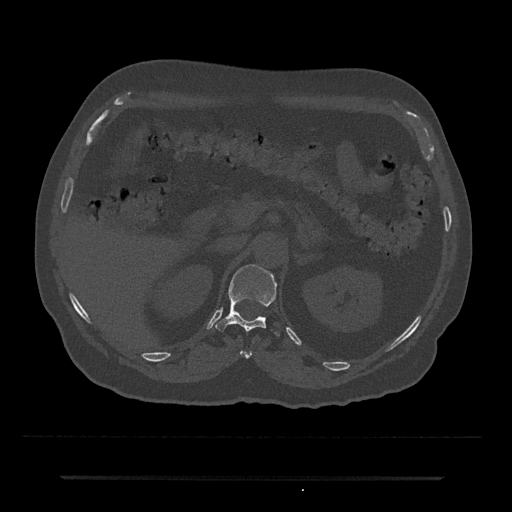
CT including the spine, one axial slice; position 128 of 797 along the scan axis; reconstruction kernel Br40s/3; 120 kVp; bone window (W 1800 / L 400 HU); 0.5 mm slice thickness; 512 × 512 image matrix, field of view 437 × 437 mm. Patient: male, 69 years. Case-level facts recorded for this patient, not image findings: primary cancer: prostate.
Annotated regions visible in this slice (semi-automatic segmentation, software-assisted and operator-edited):
- T11 vertebra: bounding box (x1, y1, x2, y2) in pixels: (240, 351, 252, 359)
- T12 vertebra: (215, 264, 280, 336)